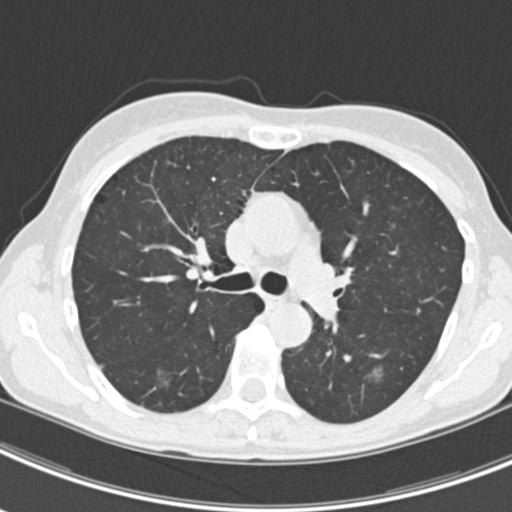
Chest CT (low-dose screening protocol), one axial image, second annual screen, lung window (W 1500 / L -600 HU), standard (soft-tissue) reconstruction kernel (B30f), slice 72 of 219 in the series. Female, age 63 years at enrolment. Current smoker at enrolment.
2 expert-annotated lung lesions on this slice (largest first), box from (x=365, y=358) to (x=405, y=393) px; (x=144, y=362)–(x=177, y=395). The screening reader recorded 9 non-calcified nodules or masses ≥4 mm on this exam (left upper lobe, right upper lobe, left upper lobe, left lower lobe, right middle lobe, left lower lobe, left lower lobe, right lower lobe, right lower lobe); which of them these boxes mark is not recorded. Official screen result: positive, other. Later outcome: lung cancer diagnosed 408 days after this screen — bronchiolo-alveolar adenocarcinoma, NOS, right upper lobe, right middle lobe, right lower lobe, left upper lobe, left lower lobe, moderately differentiated (G2), stage IV (AJCC 6th edition).